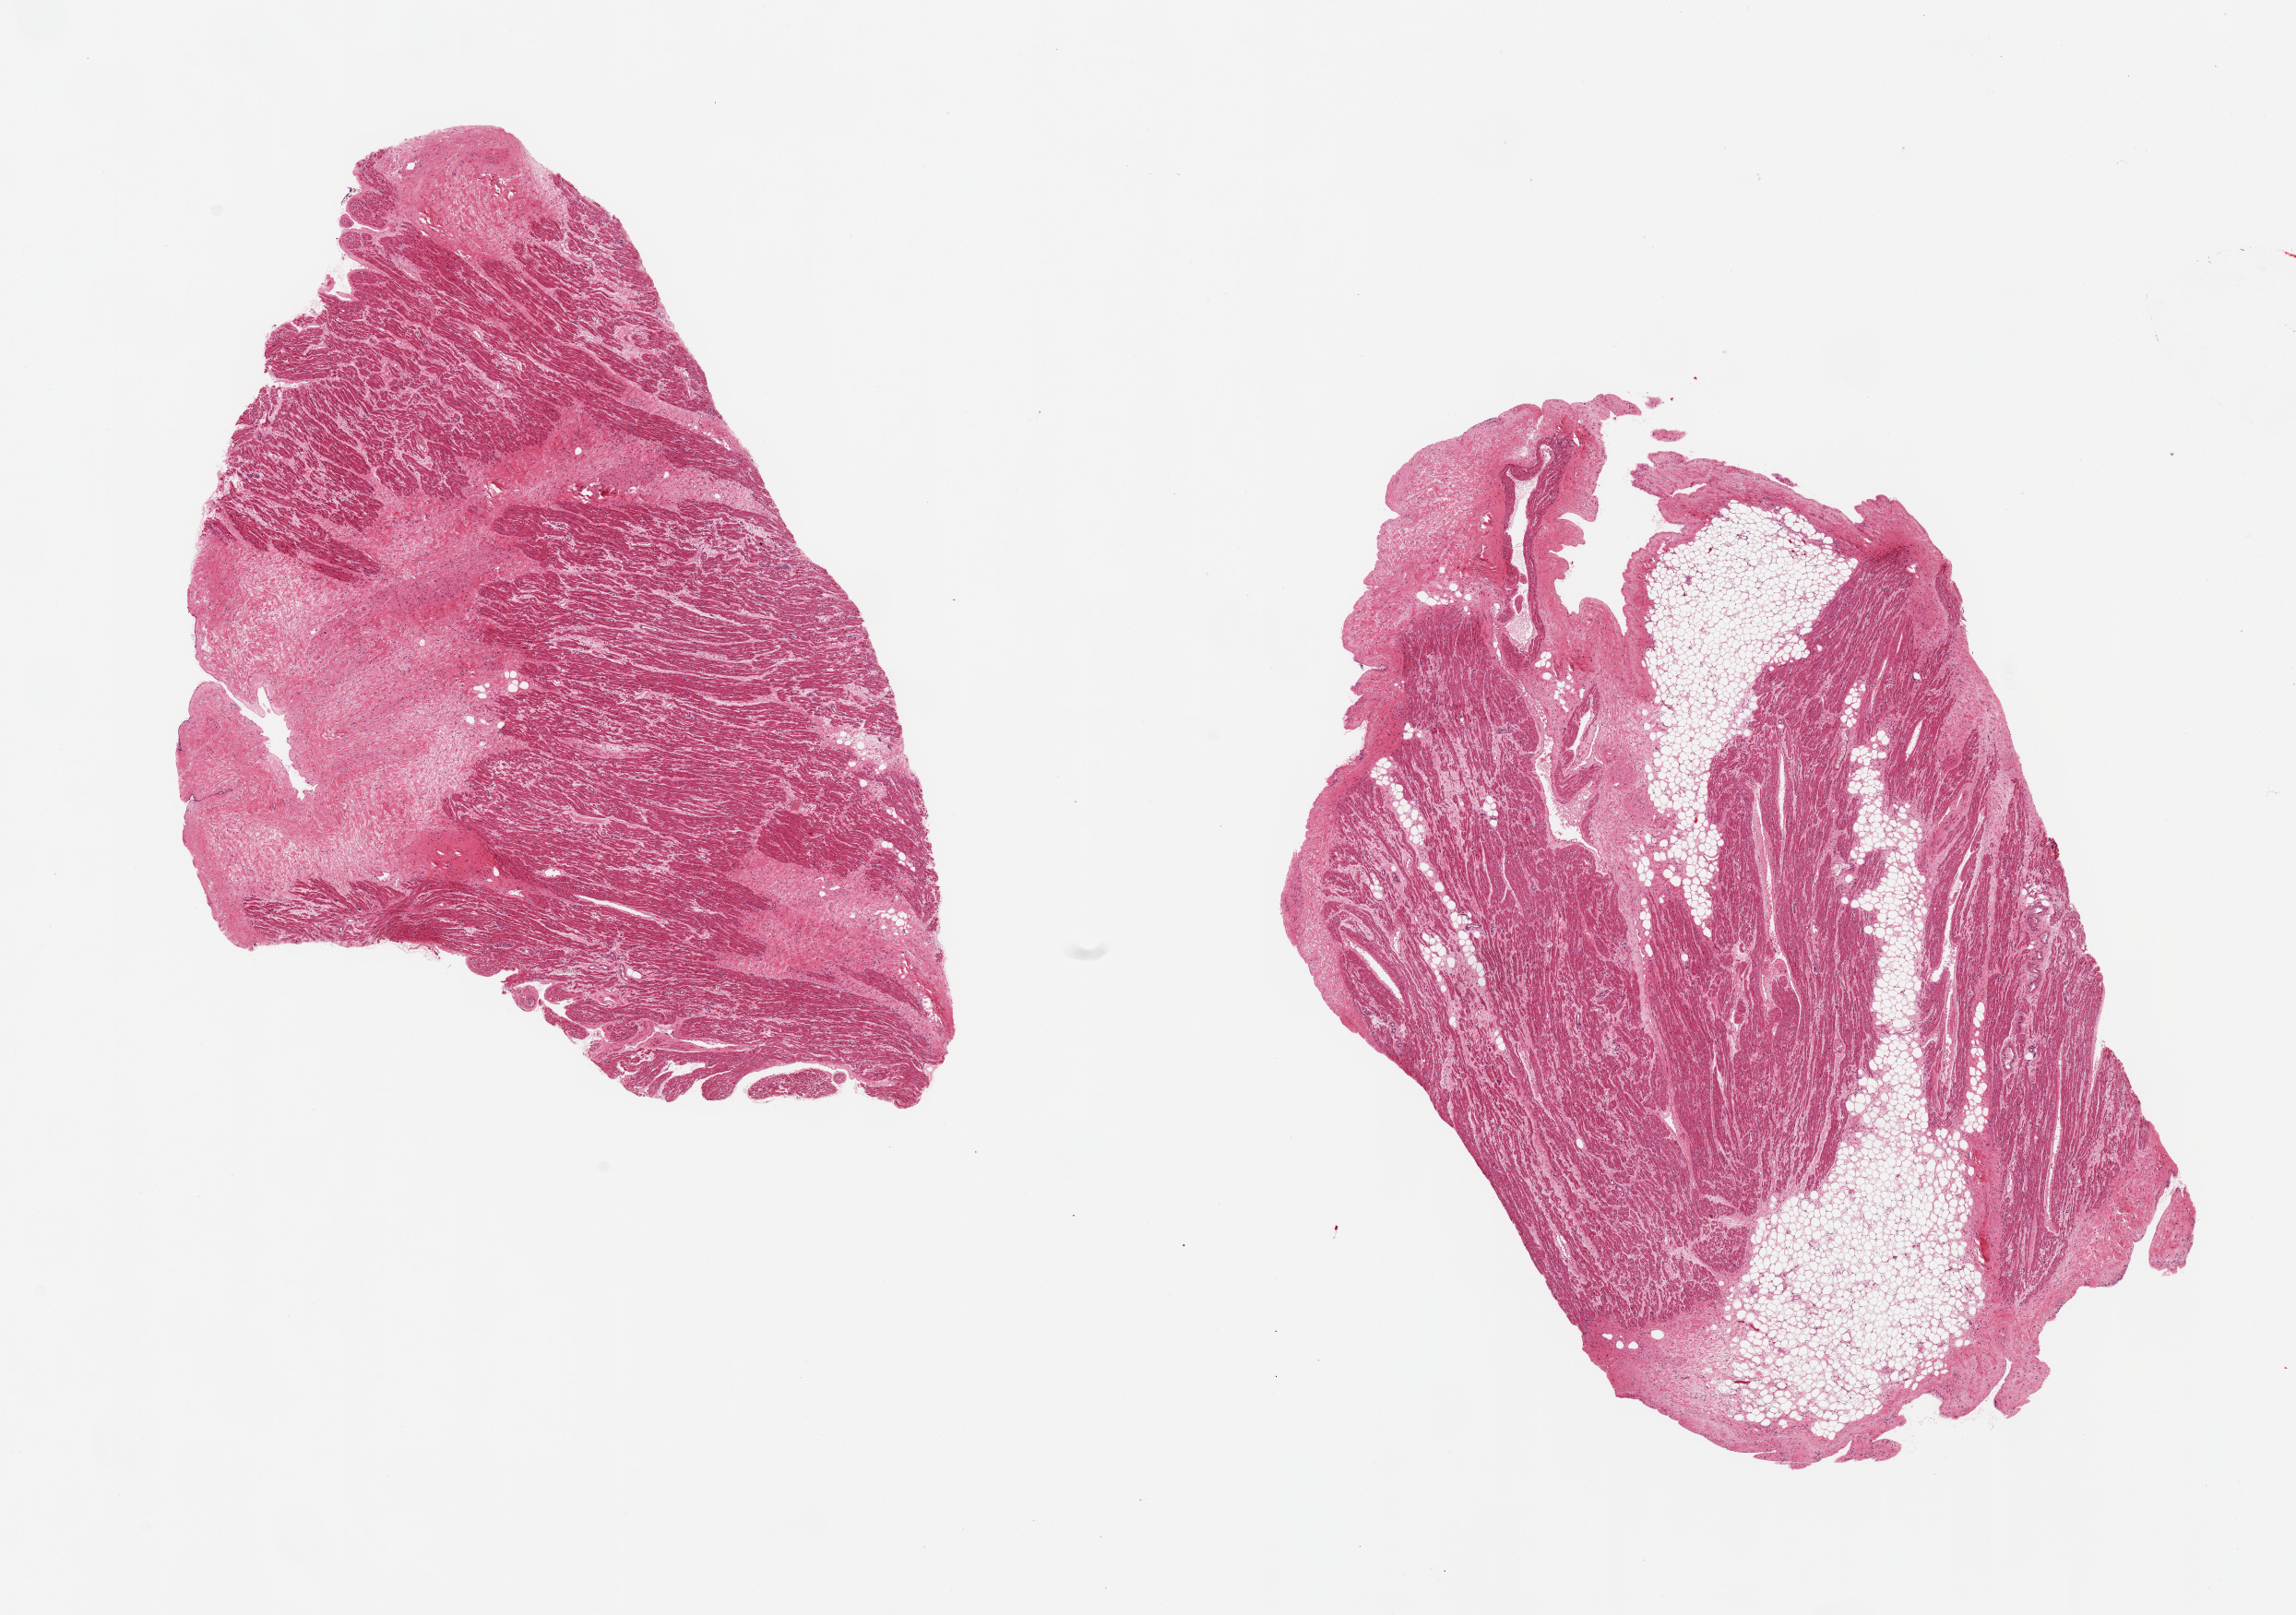
Whole-slide image, hematoxylin and eosin (H&E) stain, low-resolution overview of the scanned area, about 19.7 x 13.9 mm, PAXgene-fixed, paraffin-embedded tissue, sampled site (target tissue): auricular appendage, tissue donor sample.
Pathologist's review note for this sample: 2 pieces; 1 has 40% fibrous component; other has 40% fat.